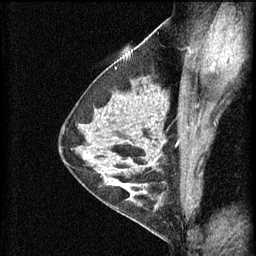
Breast MRI (dynamic contrast-enhanced), one sagittal slice; slice 38 of 60 in the series (ordered by position); 3 images stored at this slice position (order not interpretable as contrast timing); 1.5 T; TE 4.2 ms, TR 11 ms; 256 × 256 image matrix. Female patient, age 29 years.
Annotated regions visible in this slice (semi-automatic segmentation, software-assisted and operator-edited):
- analysis volume of interest (the breast-tissue region the enhancement analysis was run in; not a lesion): box from (x=105, y=172) to (x=167, y=227) px
- tumour enhancement mask (voxels above the 70 % enhancement threshold inside the analysis volume of interest): (x=108, y=172)–(x=162, y=207)